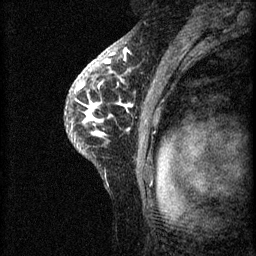
Breast MRI (dynamic contrast-enhanced), one sagittal slice; slice 46 of 60 in the series (ordered by position); 3 images stored at this slice position (order not interpretable as contrast timing); 1.5 T; TE 4.2 ms, TR 8.2 ms; 2 mm slice thickness; 256 × 256 image matrix, field of view 180 × 180 mm. Patient: female, 41 years.
Outlined on this slice (semi-automatic segmentation, software-assisted and operator-edited):
- analysis volume of interest (the breast-tissue region the enhancement analysis was run in; not a lesion): bounding box <65,62,160,175> (left, top, right, bottom; pixels)
- tumour enhancement mask (voxels above the 70 % enhancement threshold inside the analysis volume of interest): <74,62,133,137>